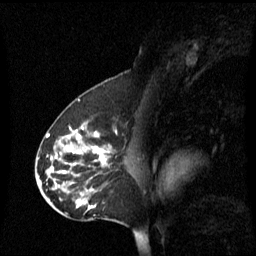
Breast MRI (dynamic contrast-enhanced), one sagittal slice. Slice 36 of 60 in the series (ordered by position). Dynamic contrast-enhanced series, image 2 of 3 at this slice position (ordered by acquisition). 1.5 T. TE 4.2 ms, TR 8.4 ms. 2.2 mm slice thickness. 256 × 256 image matrix. Female patient, age 45 years. From the clinical record (not read from this slice): setting: breast cancer imaged before/during neoadjuvant chemotherapy; receptor status: HR-positive, HER2-negative.
Annotated regions visible in this slice (semi-automatic segmentation, software-assisted and operator-edited):
- analysis volume of interest (the breast-tissue region the enhancement analysis was run in; not a lesion): bounding box [x1, y1, x2, y2] px = [38, 122, 125, 221]
- tumour enhancement mask (voxels above the 70 % enhancement threshold inside the analysis volume of interest): [50, 128, 109, 207]